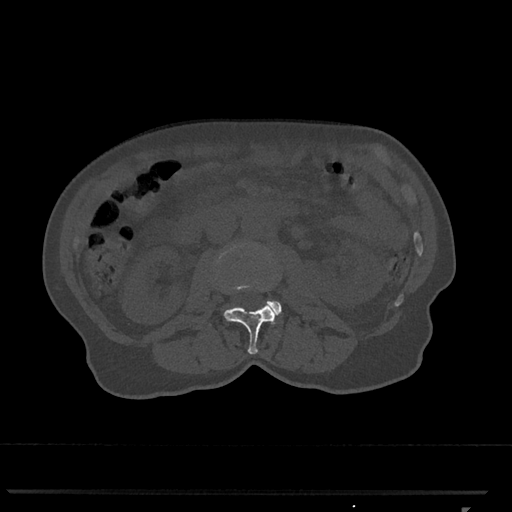
CT including the spine, one axial slice. Position 315 of 793 along the scan axis. 120 kVp. Bone window (W 1800 / L 400 HU). 0.5 mm slice thickness. 512 × 512 image matrix, field of view 380 × 380 mm. Patient: female, 62 years. From the clinical record (not read from this slice): primary cancer: renal.
Outlined on this slice (semi-automatic segmentation, software-assisted and operator-edited):
- L2 vertebra: box from (x=219, y=247) to (x=277, y=354) px
- L3 vertebra: (x=267, y=301)–(x=282, y=315)